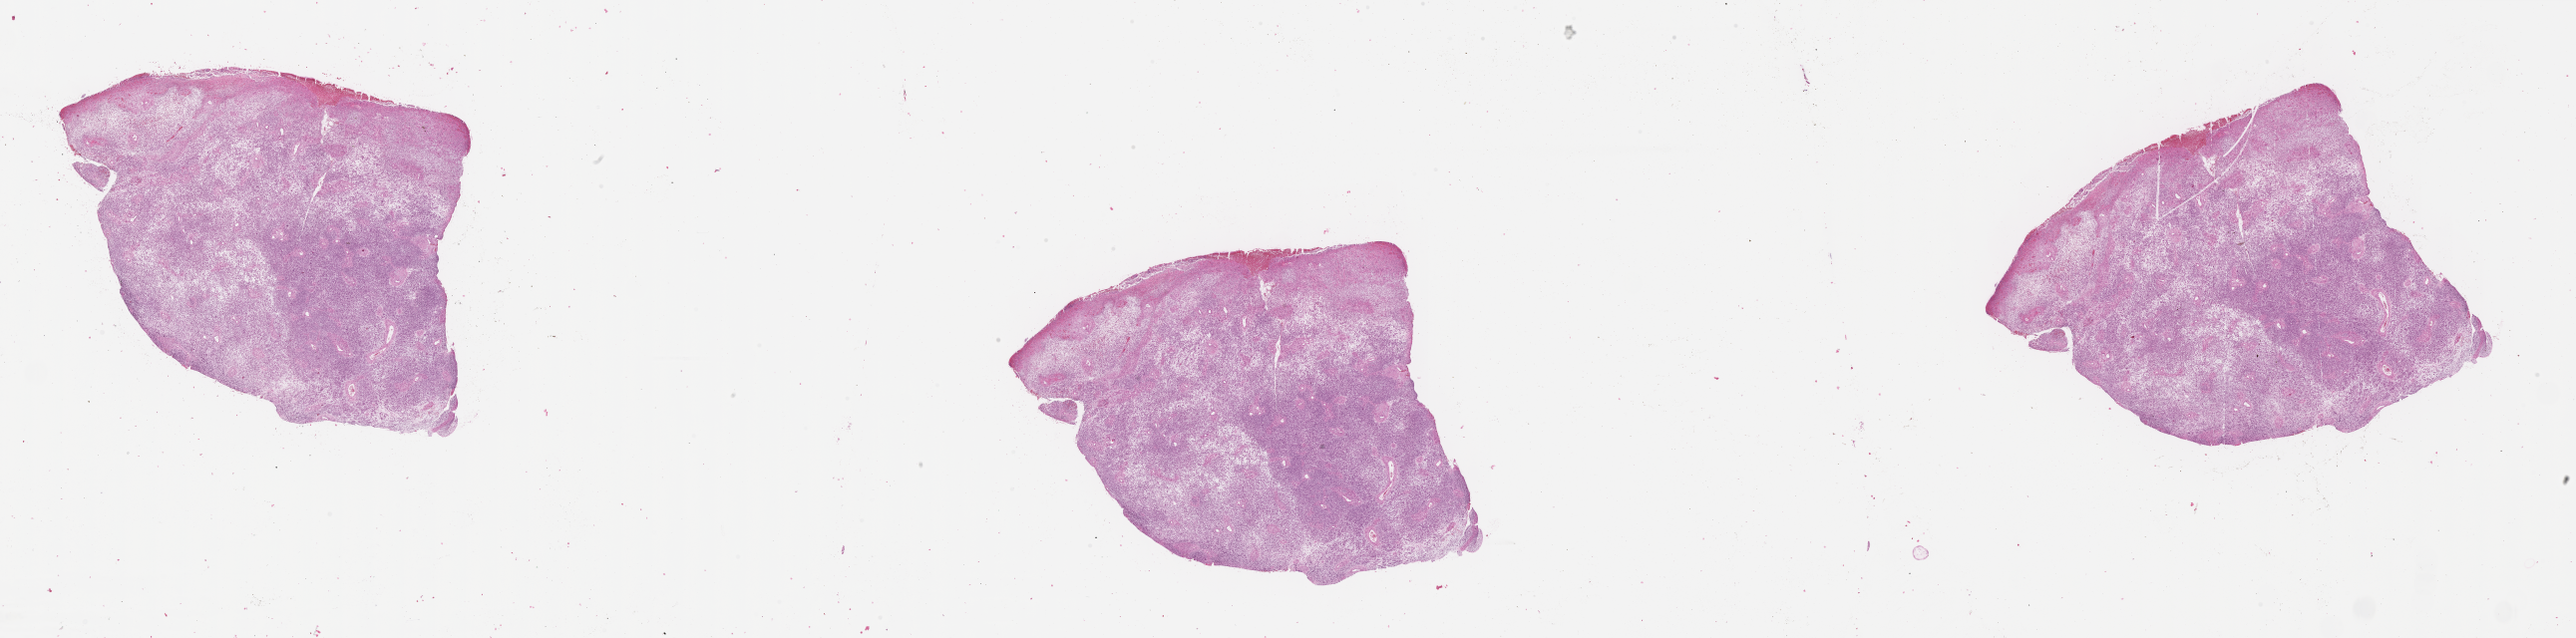
Haematoxylin and eosin whole-slide image of tumor tissue — shown as a low-resolution overview of the whole scanned area (about 41.8 x 10.3 mm). FFPE section. Site: nasopharynx. Female patient, age at diagnosis 1.8 years.
Diagnosis: rhabdomyosarcoma; histological classification: embryonal rhabdomyosarcoma.